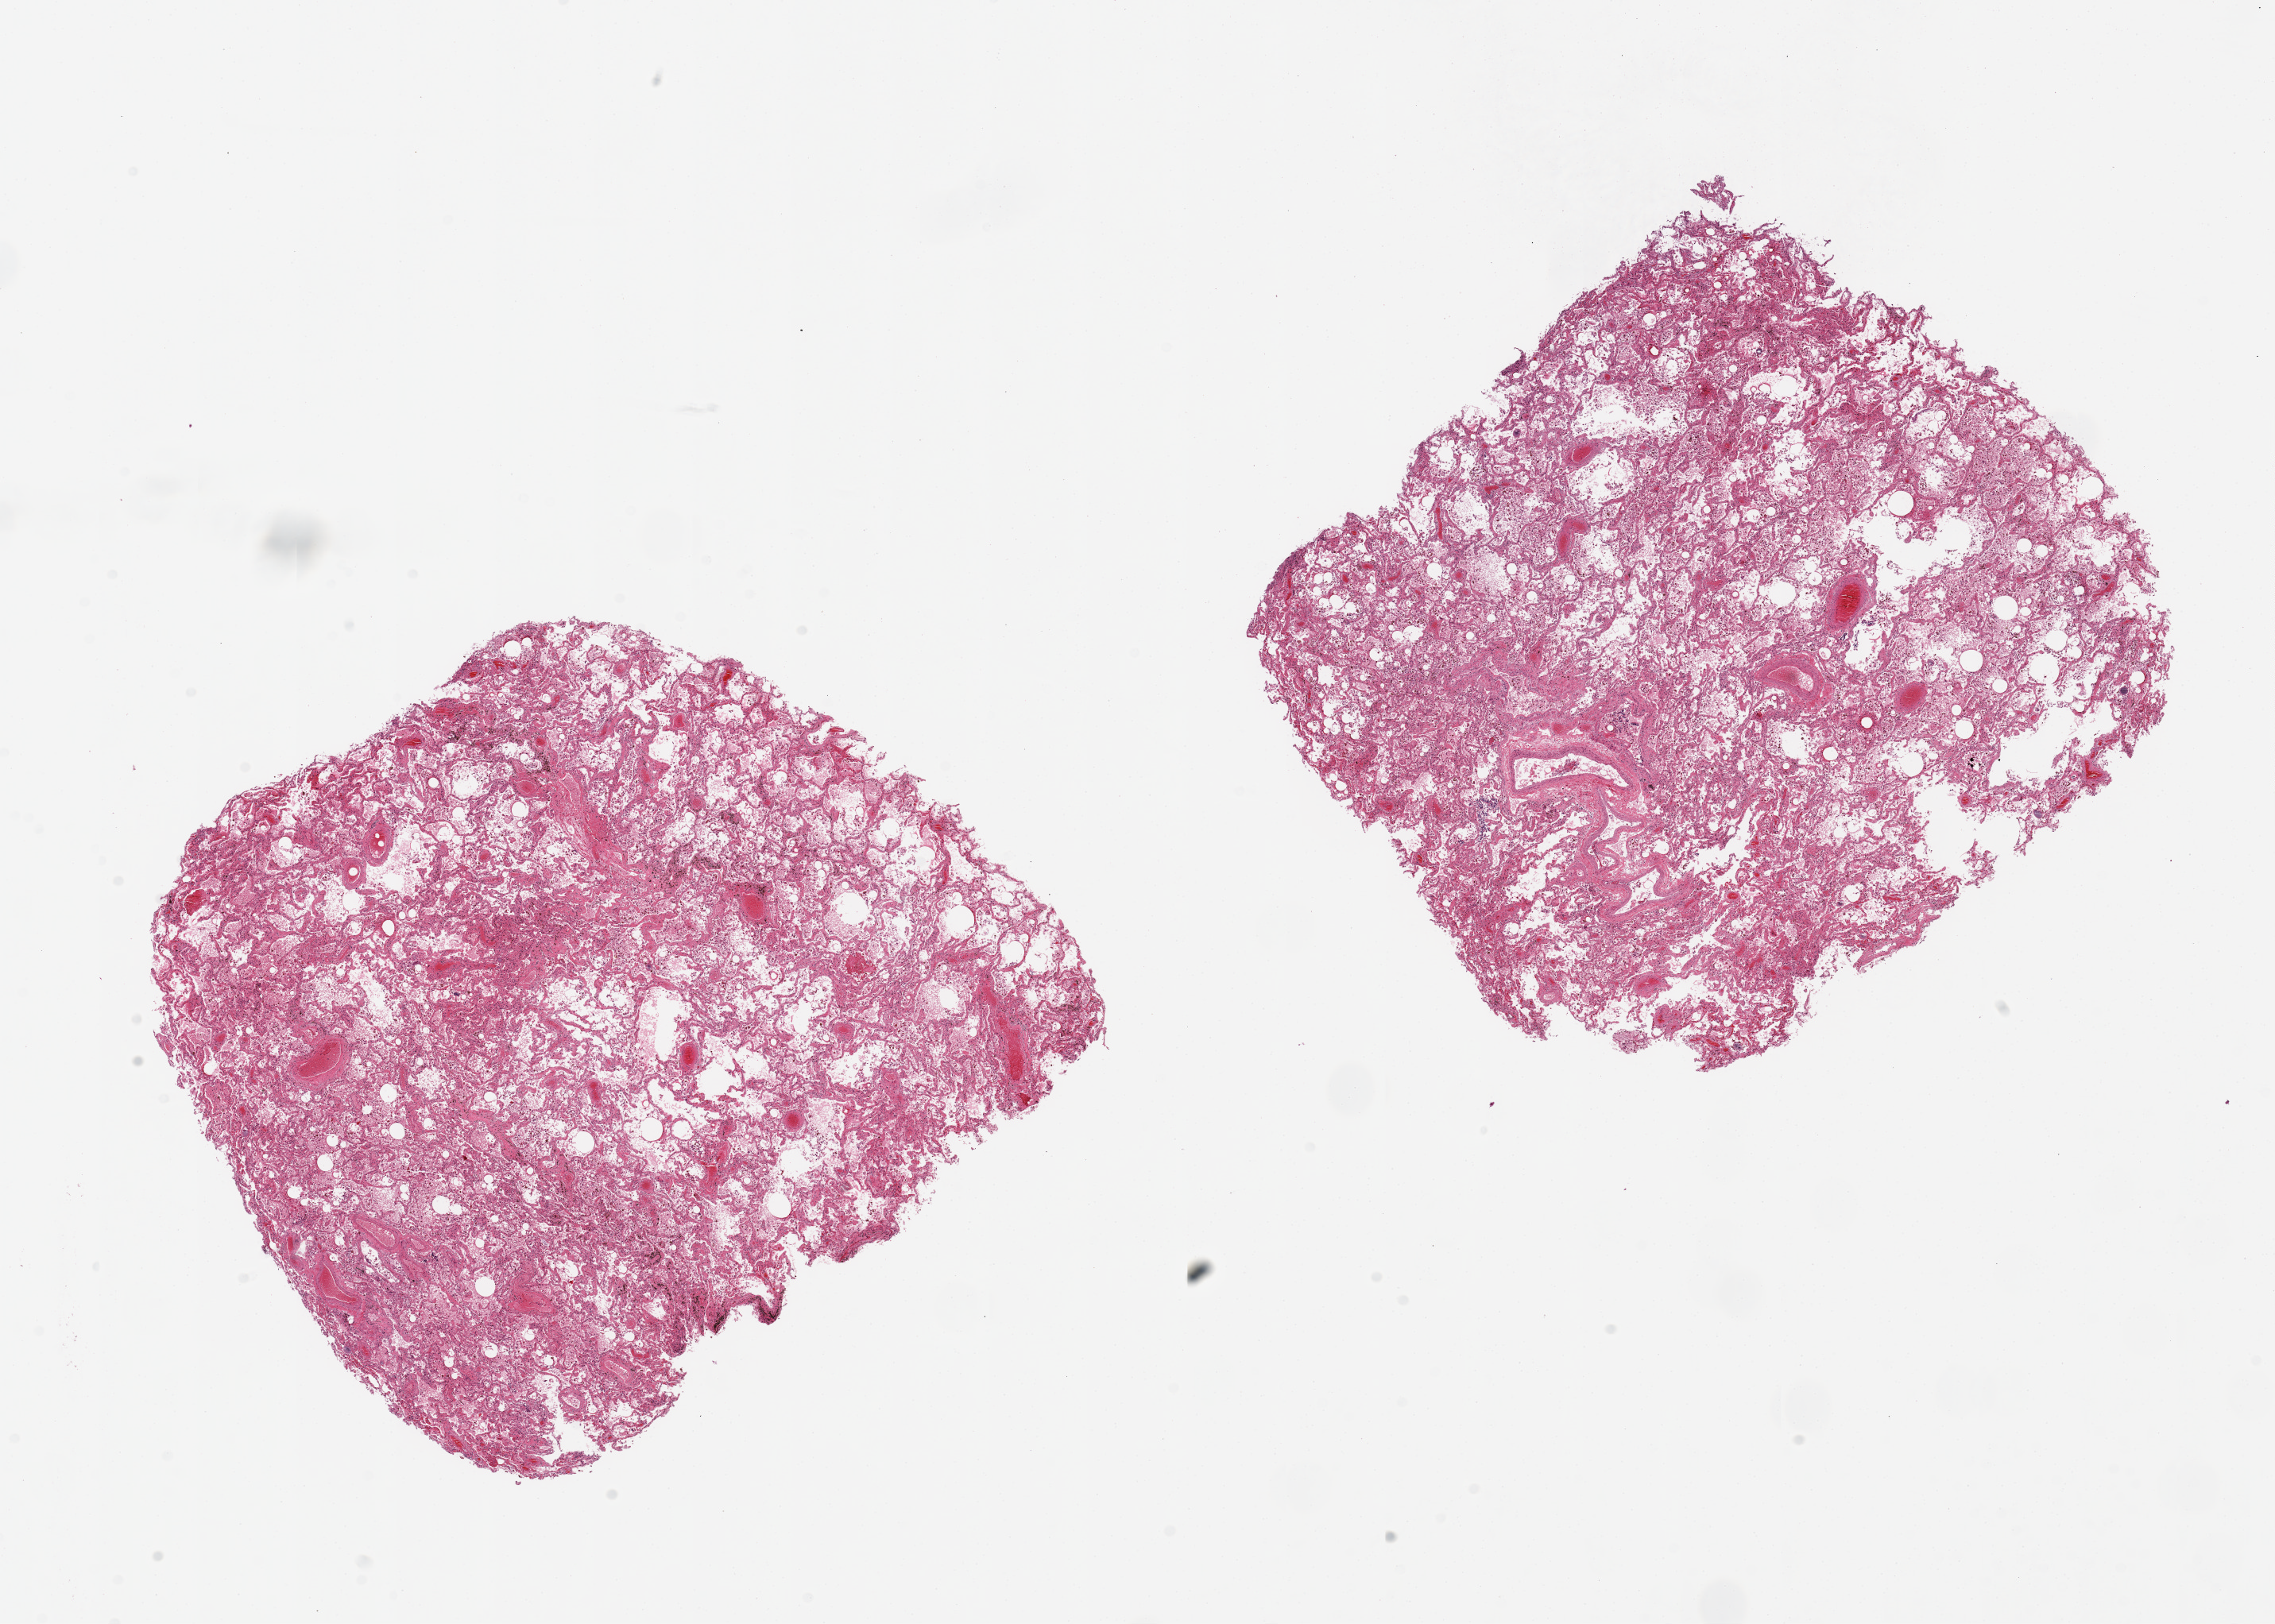
Whole-slide image, hematoxylin and eosin (H&E) stain — shown as a low-resolution overview of the whole scanned area (about 22.6 x 16.2 mm), PAXgene-fixed paraffin-embedded (PFPE) section, target tissue: lung, donor tissue sample. Donor sex: male.
Reviewer comment on this tissue sample: 2 pieces 8x7 & 7x7mm; badly autolyzed, apparent emphysematous changes.